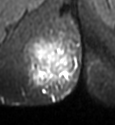
MRI of an extremity soft-tissue mass, one axial slice. Position 15 of 49 along the scan axis. STIR. MR volume resampled by the dataset authors to the PET/CT grid (not the native acquisition matrix). 115 × 125 image matrix, field of view 112 × 122 mm. Female patient. From the clinical record (not read from this slice): histological type: epithelioid sarcoma; grade: intermediate; site of the primary tumour: right buttock.
Outlined on this slice (expert contour drawn on MRI and transferred to this co-registered scan by the dataset authors):
- gross tumour volume including surrounding oedema: bounding box [x1, y1, x2, y2] px = [22, 28, 80, 101]
- gross tumour volume (mass): [31, 39, 64, 67]